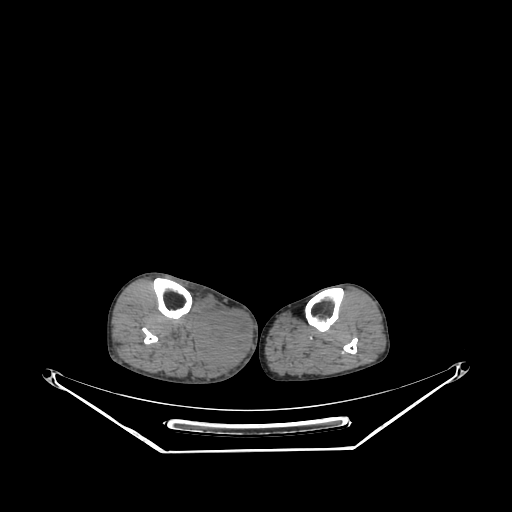
CT of an extremity soft-tissue mass (from a PET/CT study), one axial slice. Slice 139 of 267 in the series (ordered by position). Reconstruction kernel SOFT. Soft-tissue window (W 400 / L 40 HU). 3.75 mm slice thickness. 512 × 512 image matrix, field of view 500 × 500 mm. Male patient. From the clinical record (not read from this slice): histological type: pleiomorphic liposarcoma; grade: high; site of the primary tumour: right calf.
Outlined on this slice (expert contour drawn on MRI and transferred to this co-registered scan by the dataset authors):
- gross tumour volume including surrounding oedema: bounding box (x1, y1, x2, y2) in pixels: (196, 306, 250, 368)
- gross tumour volume (mass): (196, 308, 250, 364)